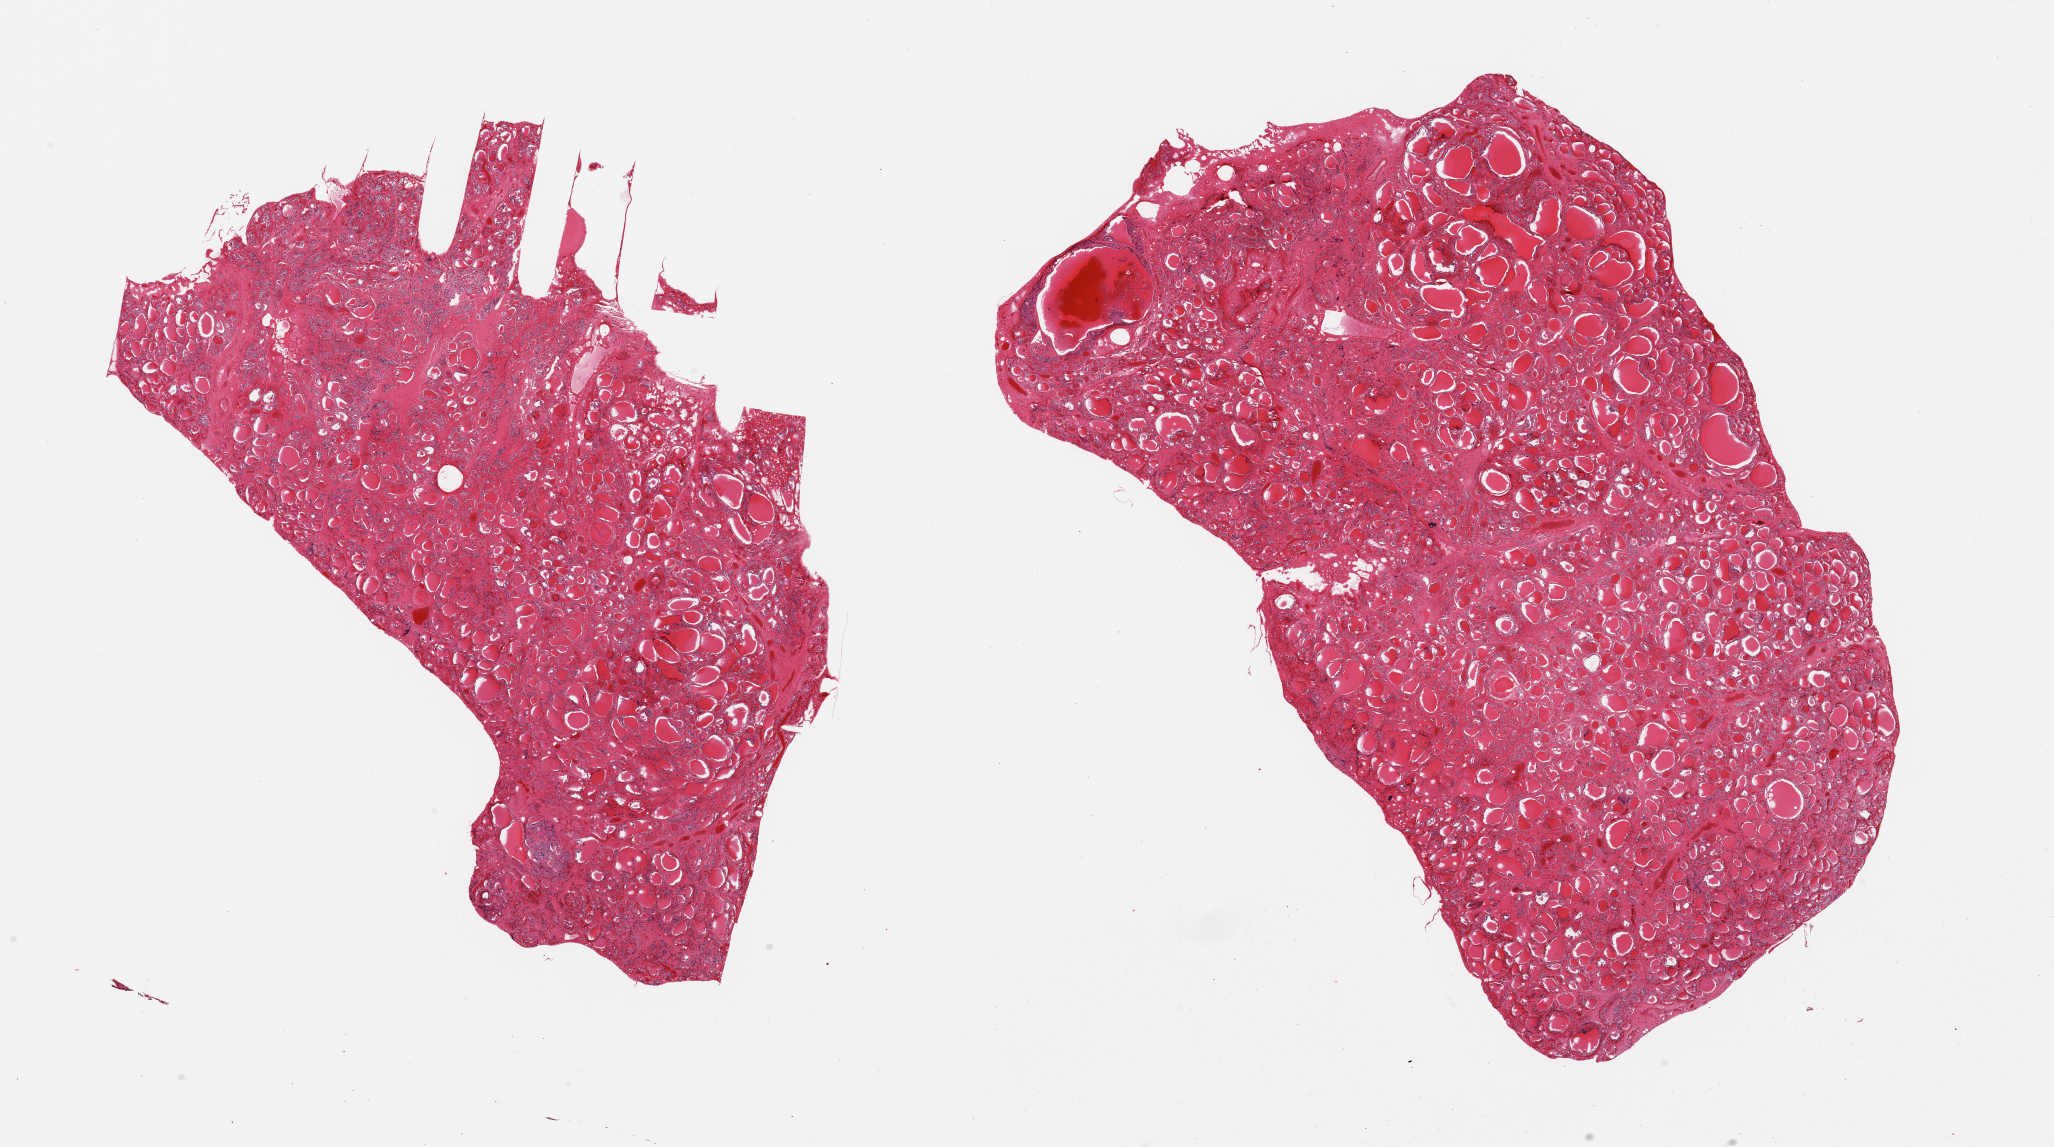
Haematoxylin and eosin whole-slide image, shown as a low-resolution overview of the whole scanned area (about 32.5 x 18.1 mm); PAXgene-fixed paraffin-embedded (PFPE) section; sampled site (target tissue): thyroid; tissue donor sample. Donor sex: male.
Reviewer comment on this tissue sample: 2 pieces.